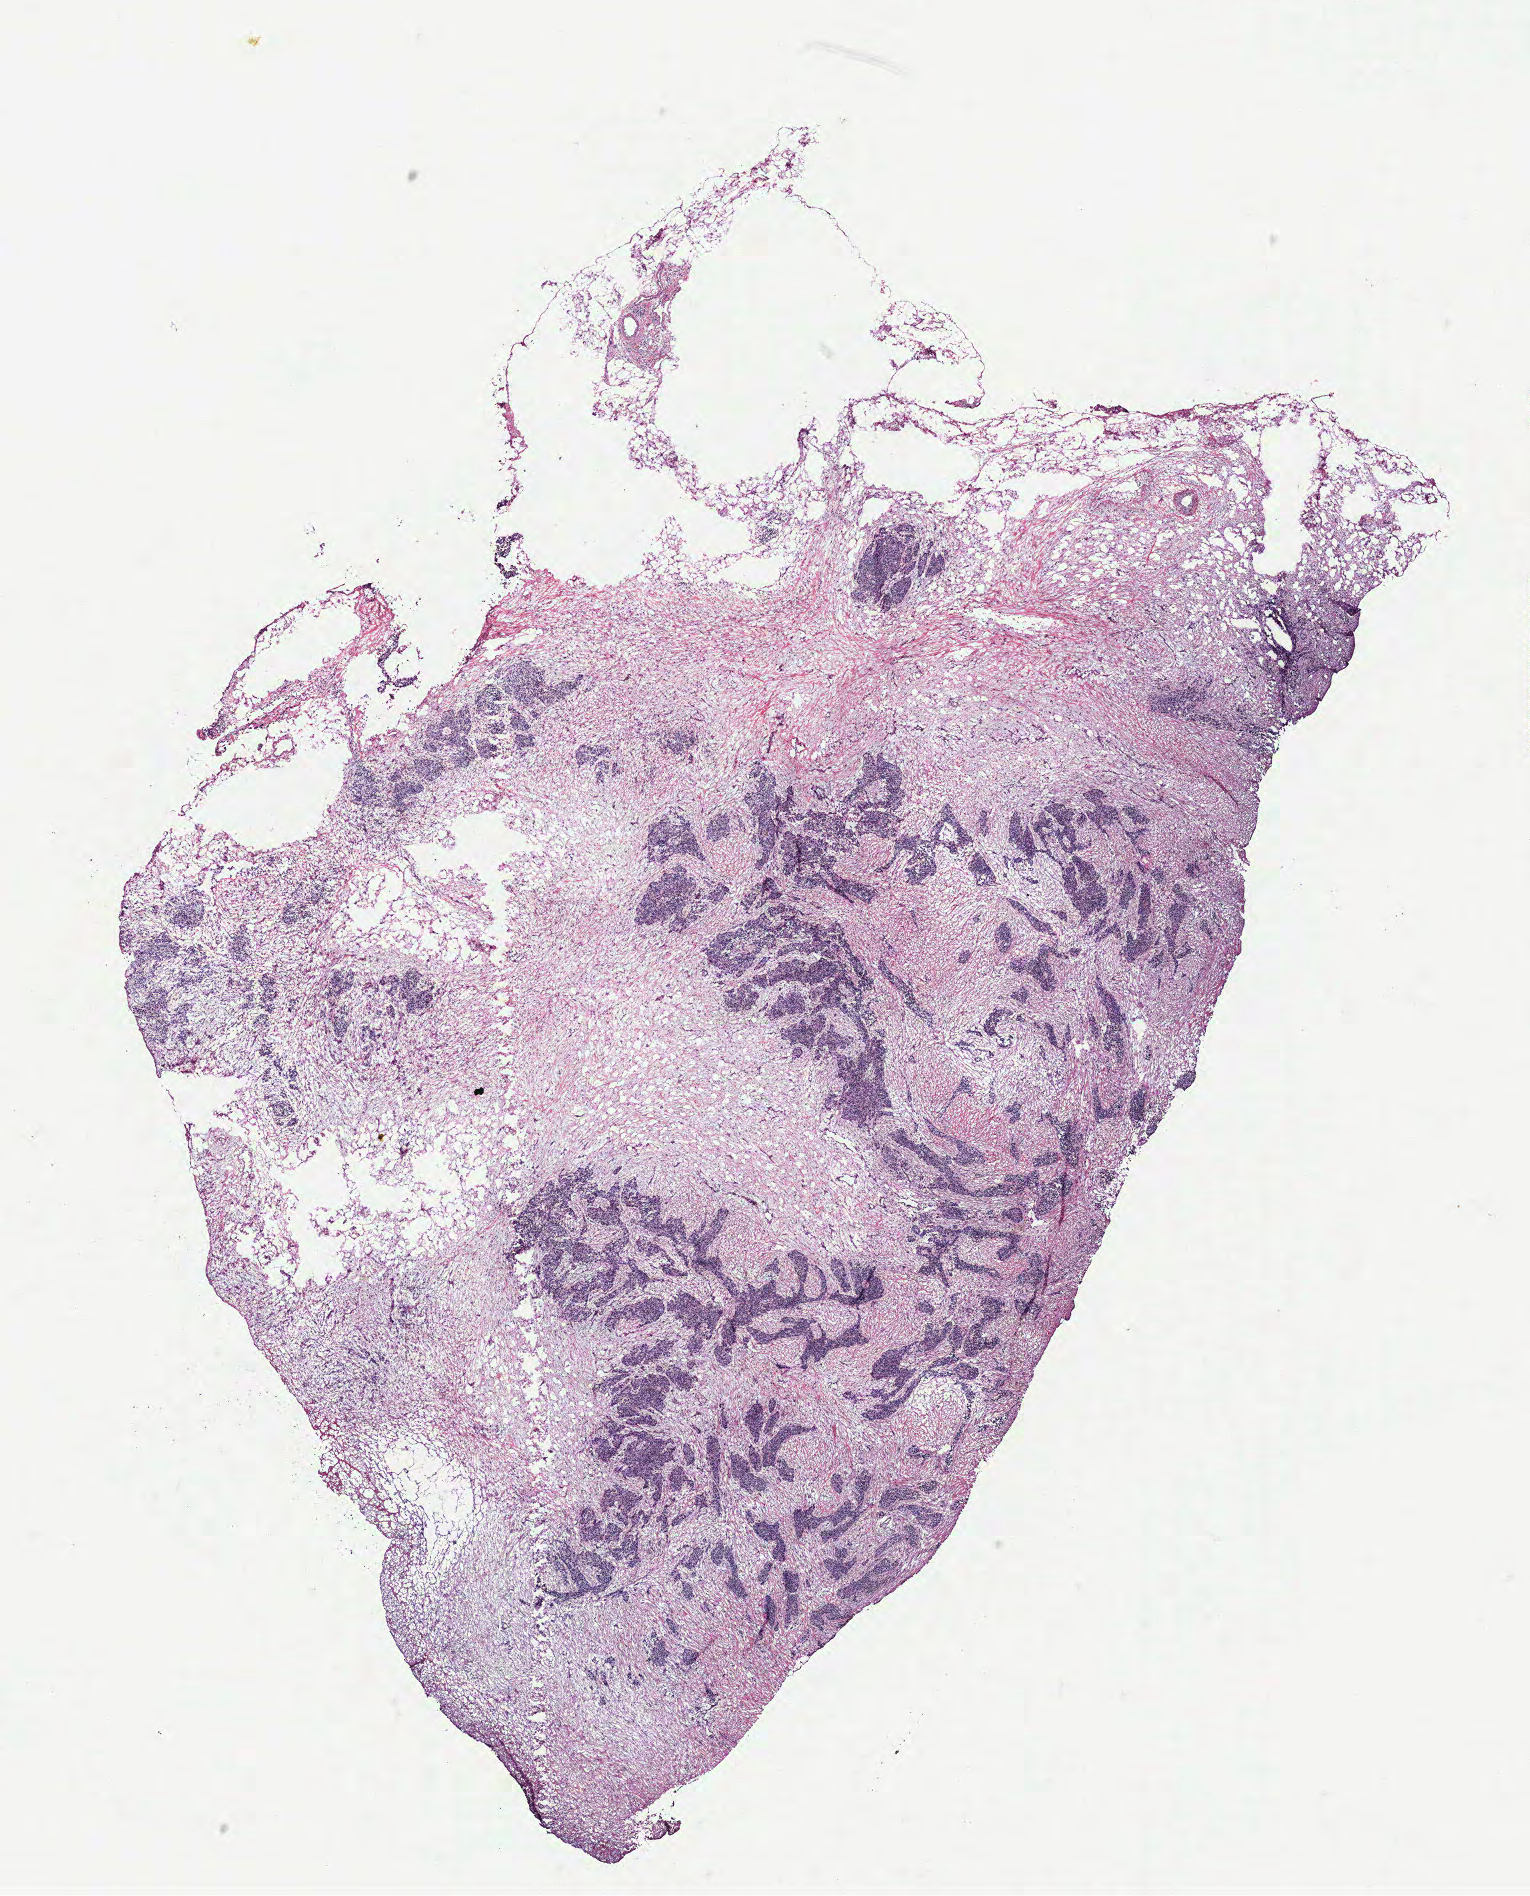
Digitized H&E-stained tissue section (whole slide) — a low-resolution overview of the entire scanned area, about 12.2 x 15.2 mm (from a 40x scan), ovary, tumour tissue. 70-year-old female patient.
Diagnosis: Serous adenocarcinoma, NOS (peritoneum, NOS).